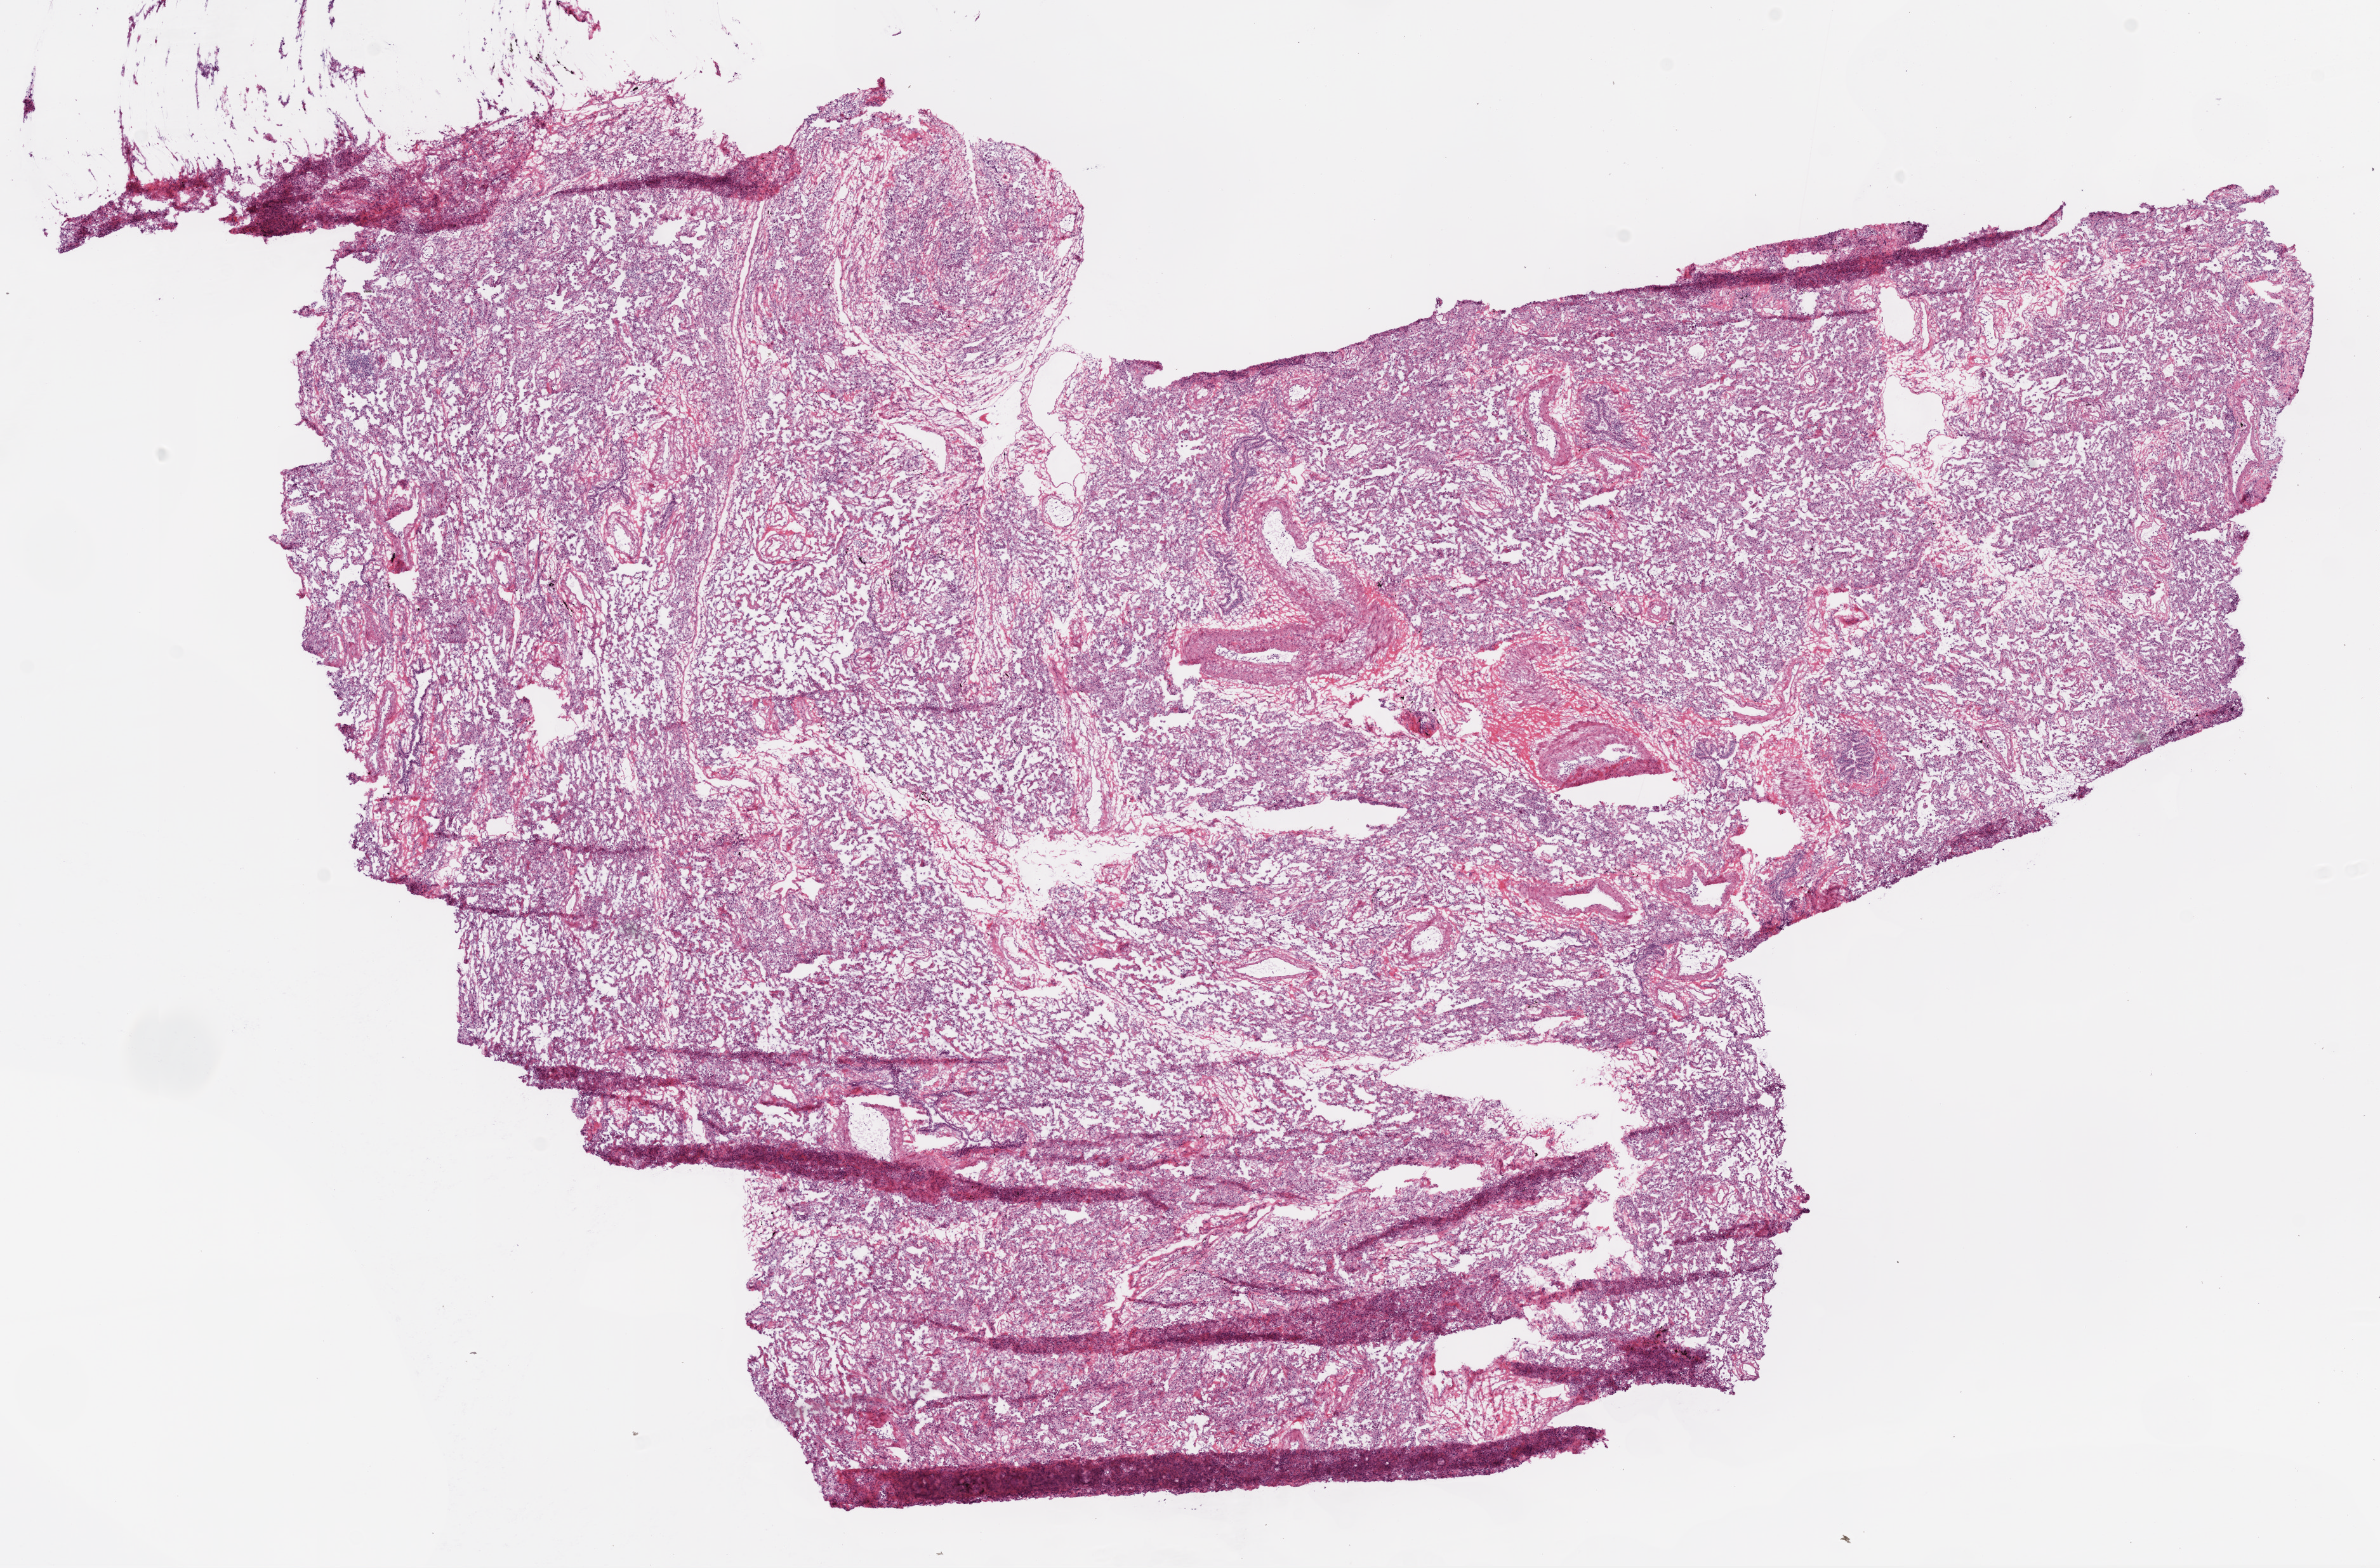
Digitized H&E tissue section (whole slide) — shown as a low-resolution overview of the whole scanned area (about 15.0 x 9.9 mm, acquisition: 20x scan); frozen section; solid tissue normal (non-tumour tissue) sample from the lung. Patient: female, age at initial diagnosis 76 years.
This section: solid tissue normal (non-tumour) sample from the same patient. Patient diagnosis: Squamous cell carcinoma, NOS (lower lobe, lung).